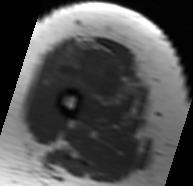
MRI of an extremity soft-tissue mass, one axial slice; position 25 of 91 along the scan axis; MR volume resampled by the dataset authors to the PET/CT grid (not the native acquisition matrix); 3.27 mm slice thickness; 193 × 186 image matrix, field of view 188 × 182 mm. Female patient. Case-level facts recorded for this patient, not image findings: histological type: malignant solitary fibrous tumor; grade: intermediate; site of the primary tumour: right thigh.
Structures marked on this image (expert contour drawn on MRI and transferred to this co-registered scan by the dataset authors):
- gross tumour volume including surrounding oedema: bounding box [x1, y1, x2, y2] px = [47, 37, 144, 109]
- gross tumour volume (mass): [54, 48, 125, 100]